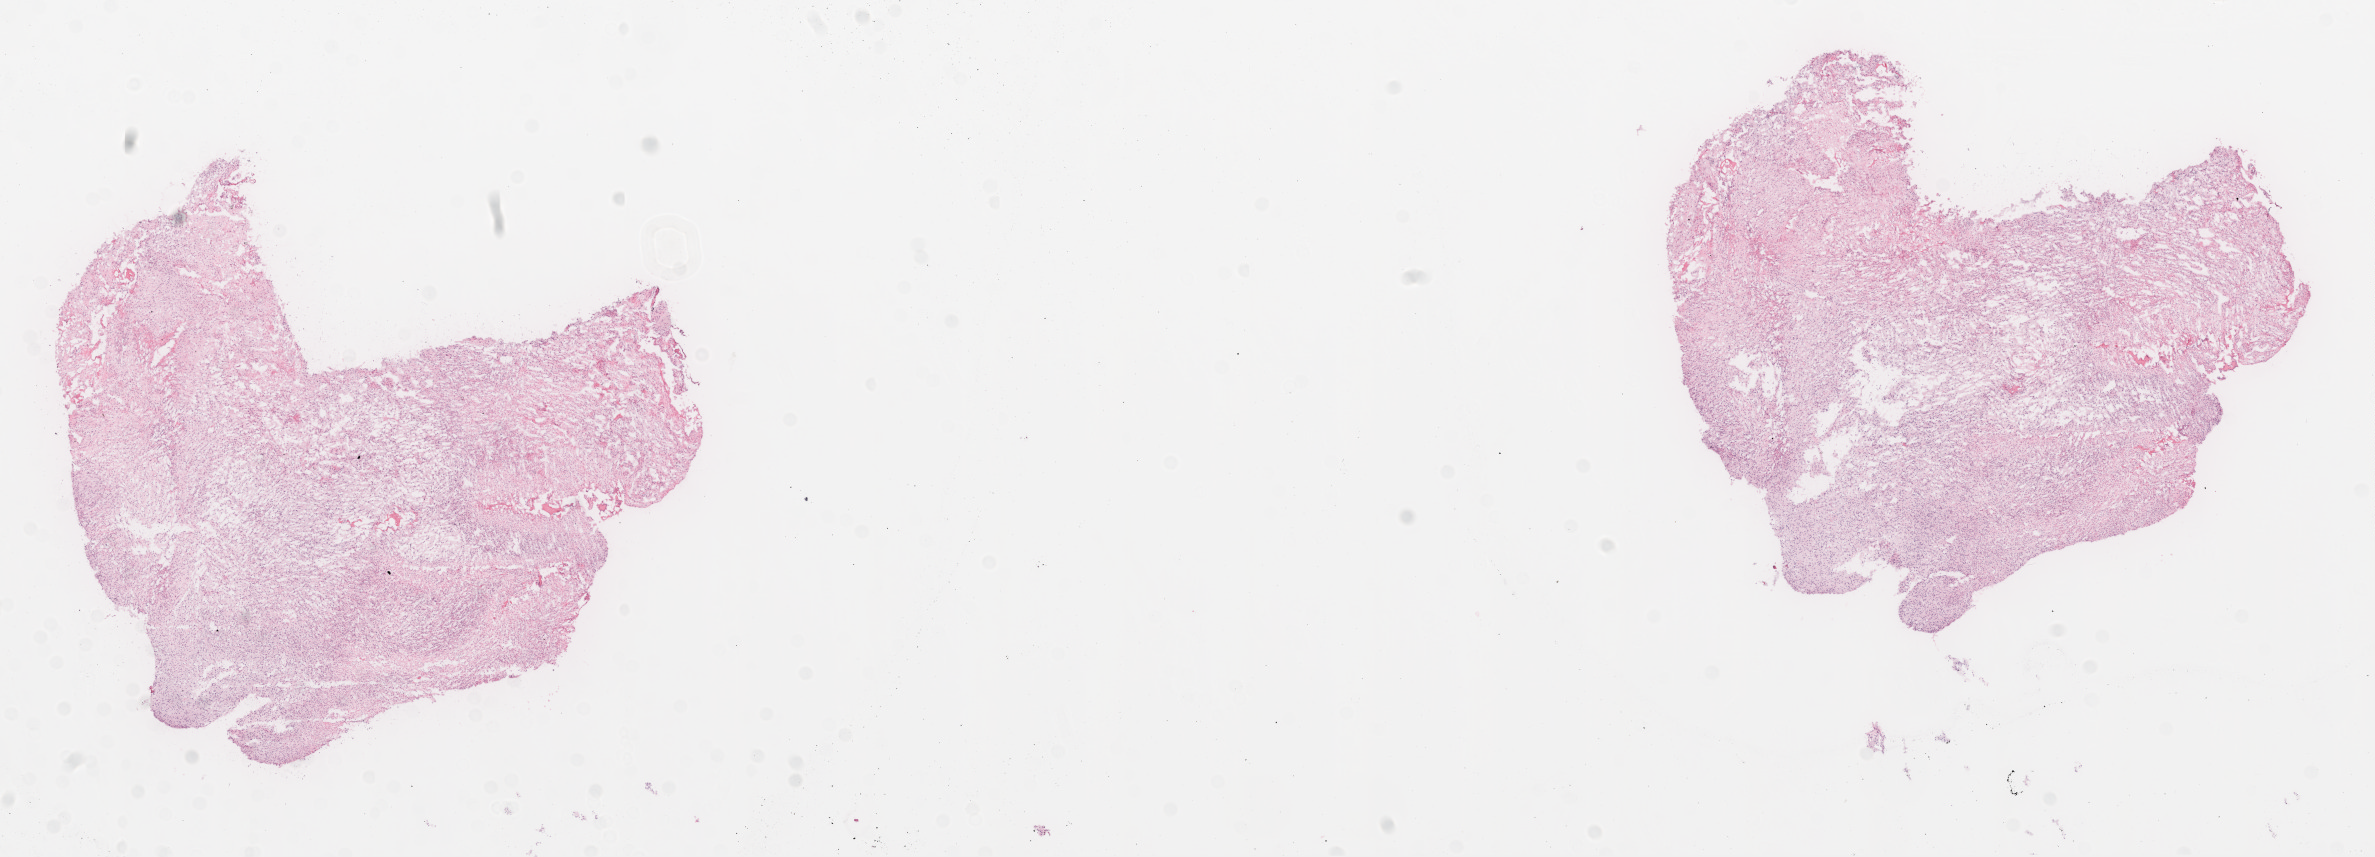
Whole-slide histology image, H&E, a low-resolution overview of the entire scanned area, about 19.1 x 6.9 mm (slide scanned at 20x); frozen section from the top of the tissue portion; sample: primary tumour, brain. Male, age 83 years at initial diagnosis. Pathologist review of this section (percent, as recorded): tumour cells 98%, tumour nuclei 85%, normal cells 0%, stromal cells 0%, necrosis 2%.
* pathologic diagnosis: Glioblastoma